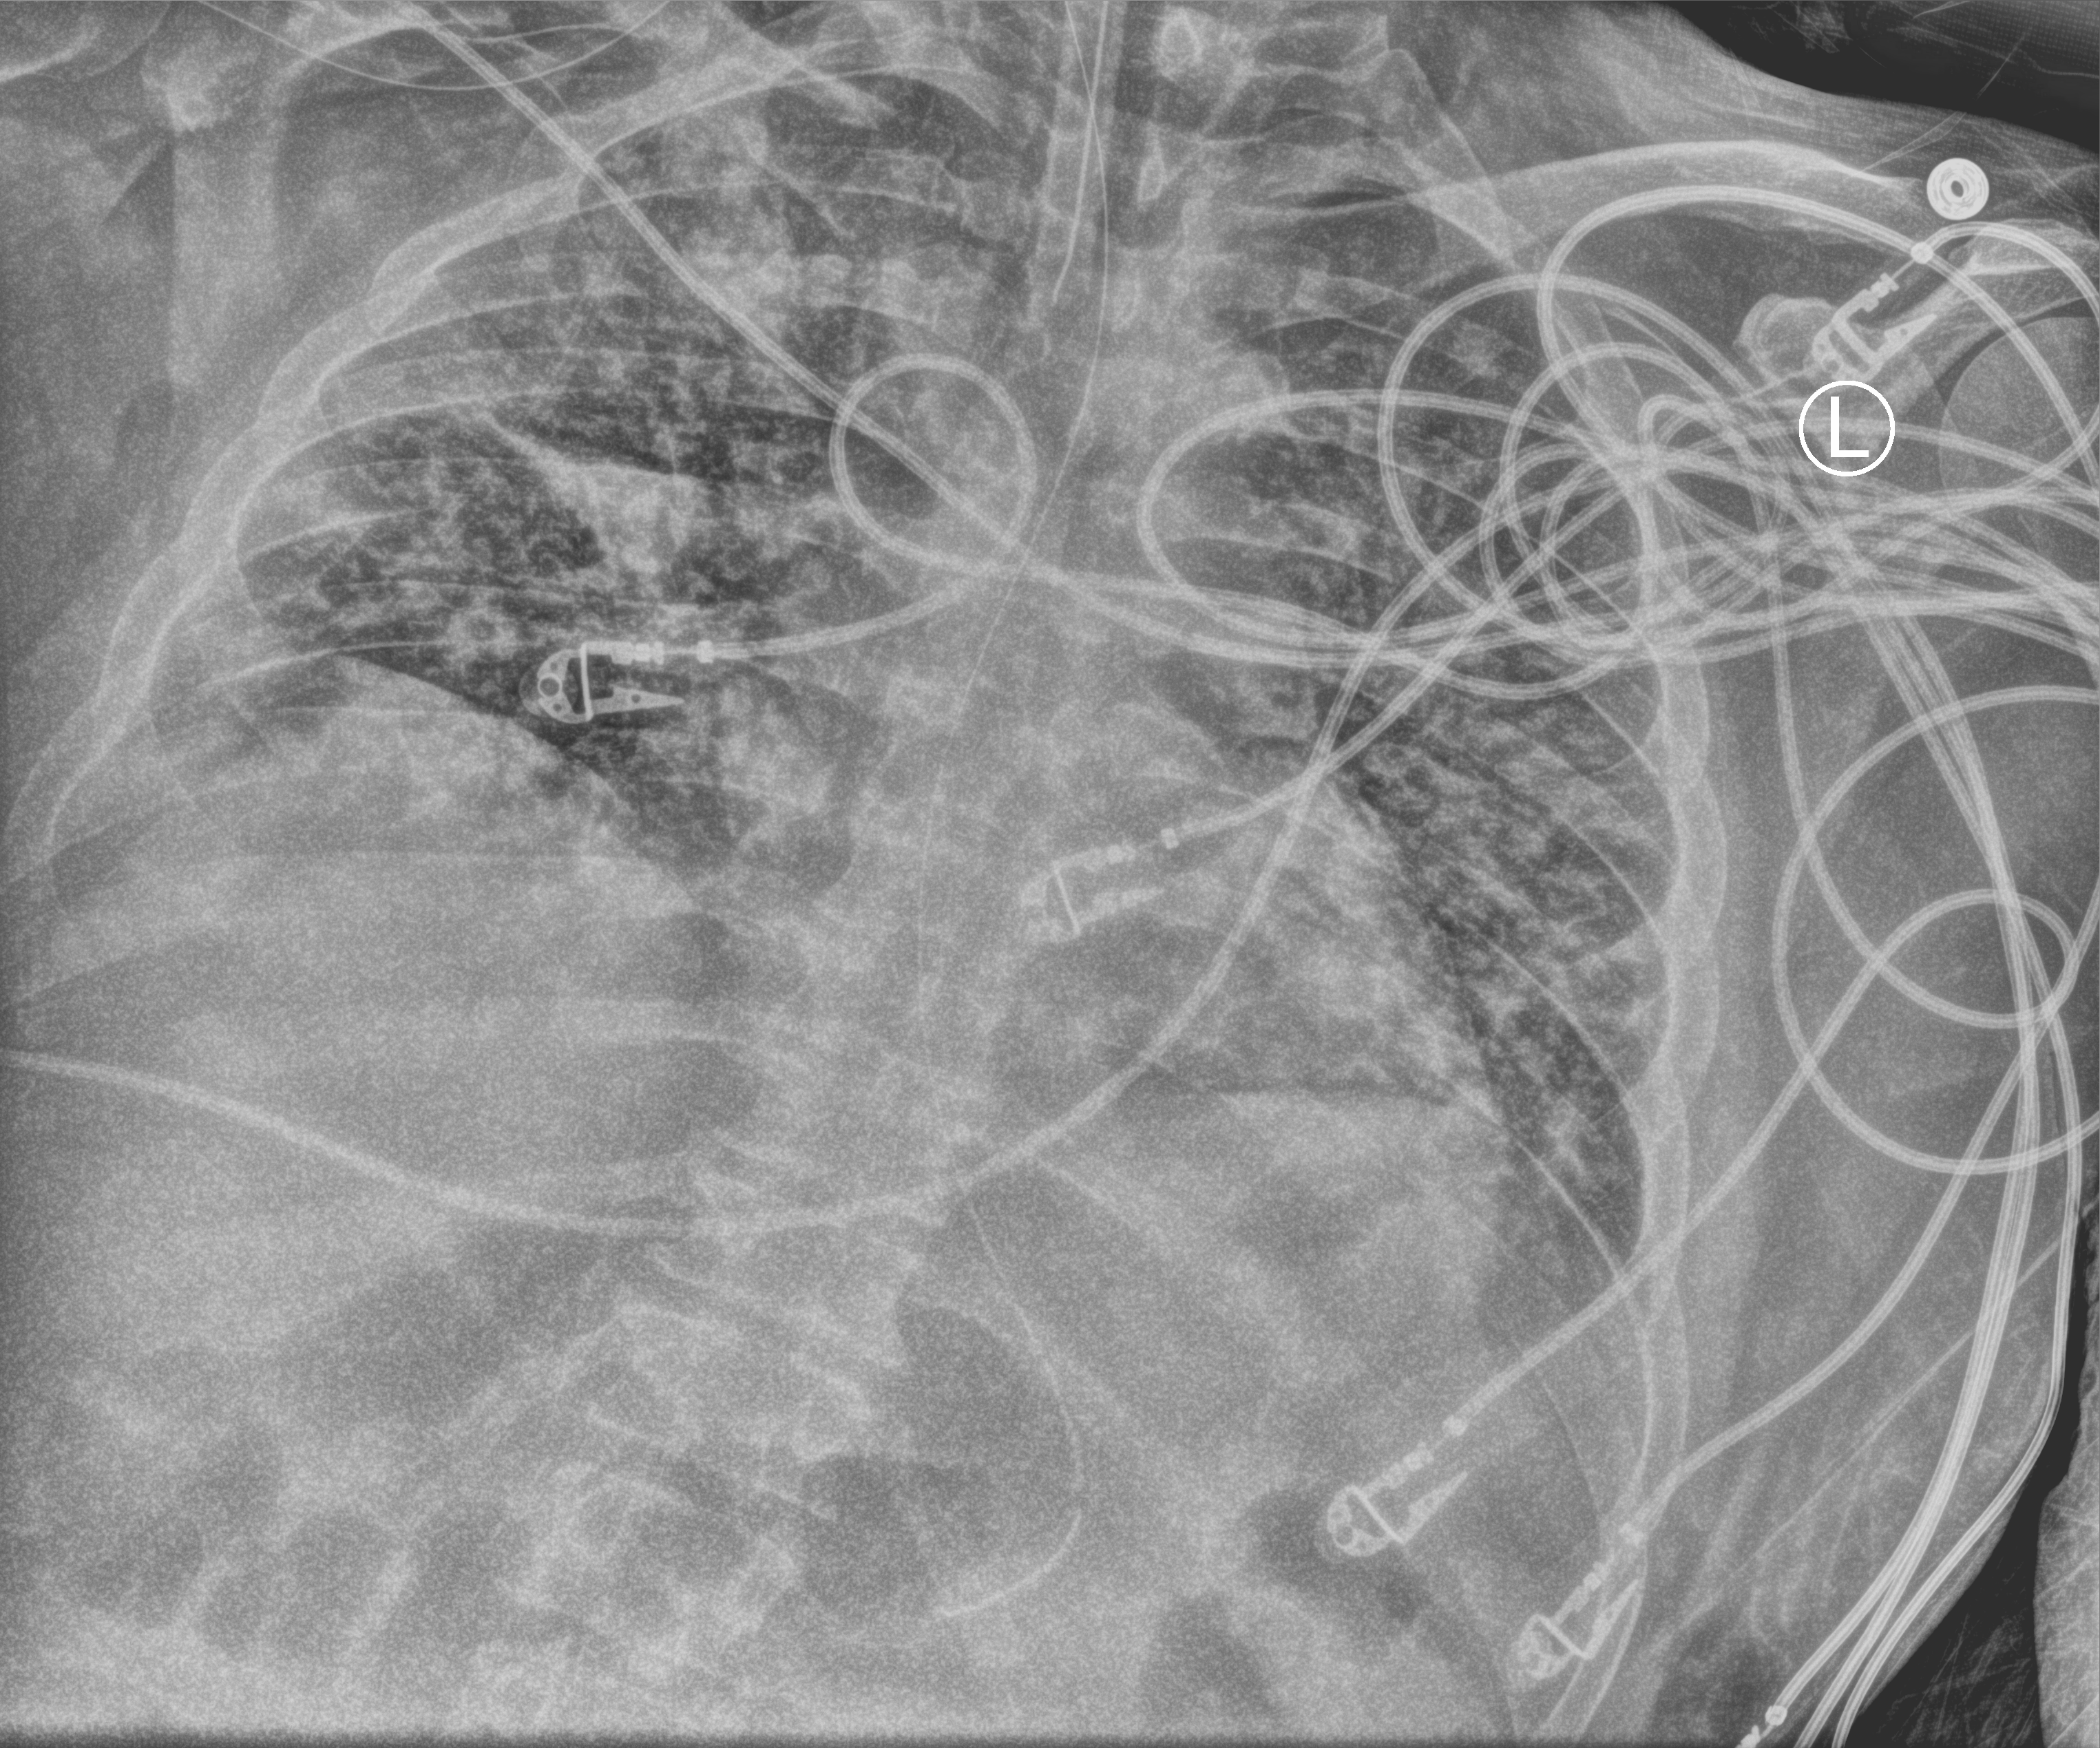
Chest X-ray (portable). Patient hospitalised with COVID-19, aged 18–59 years.
Admission-level facts for this patient (not findings on this image; timing relative to this image not recorded): admitted to intensive care during this hospital stay: yes; length of hospital stay: 31 days.